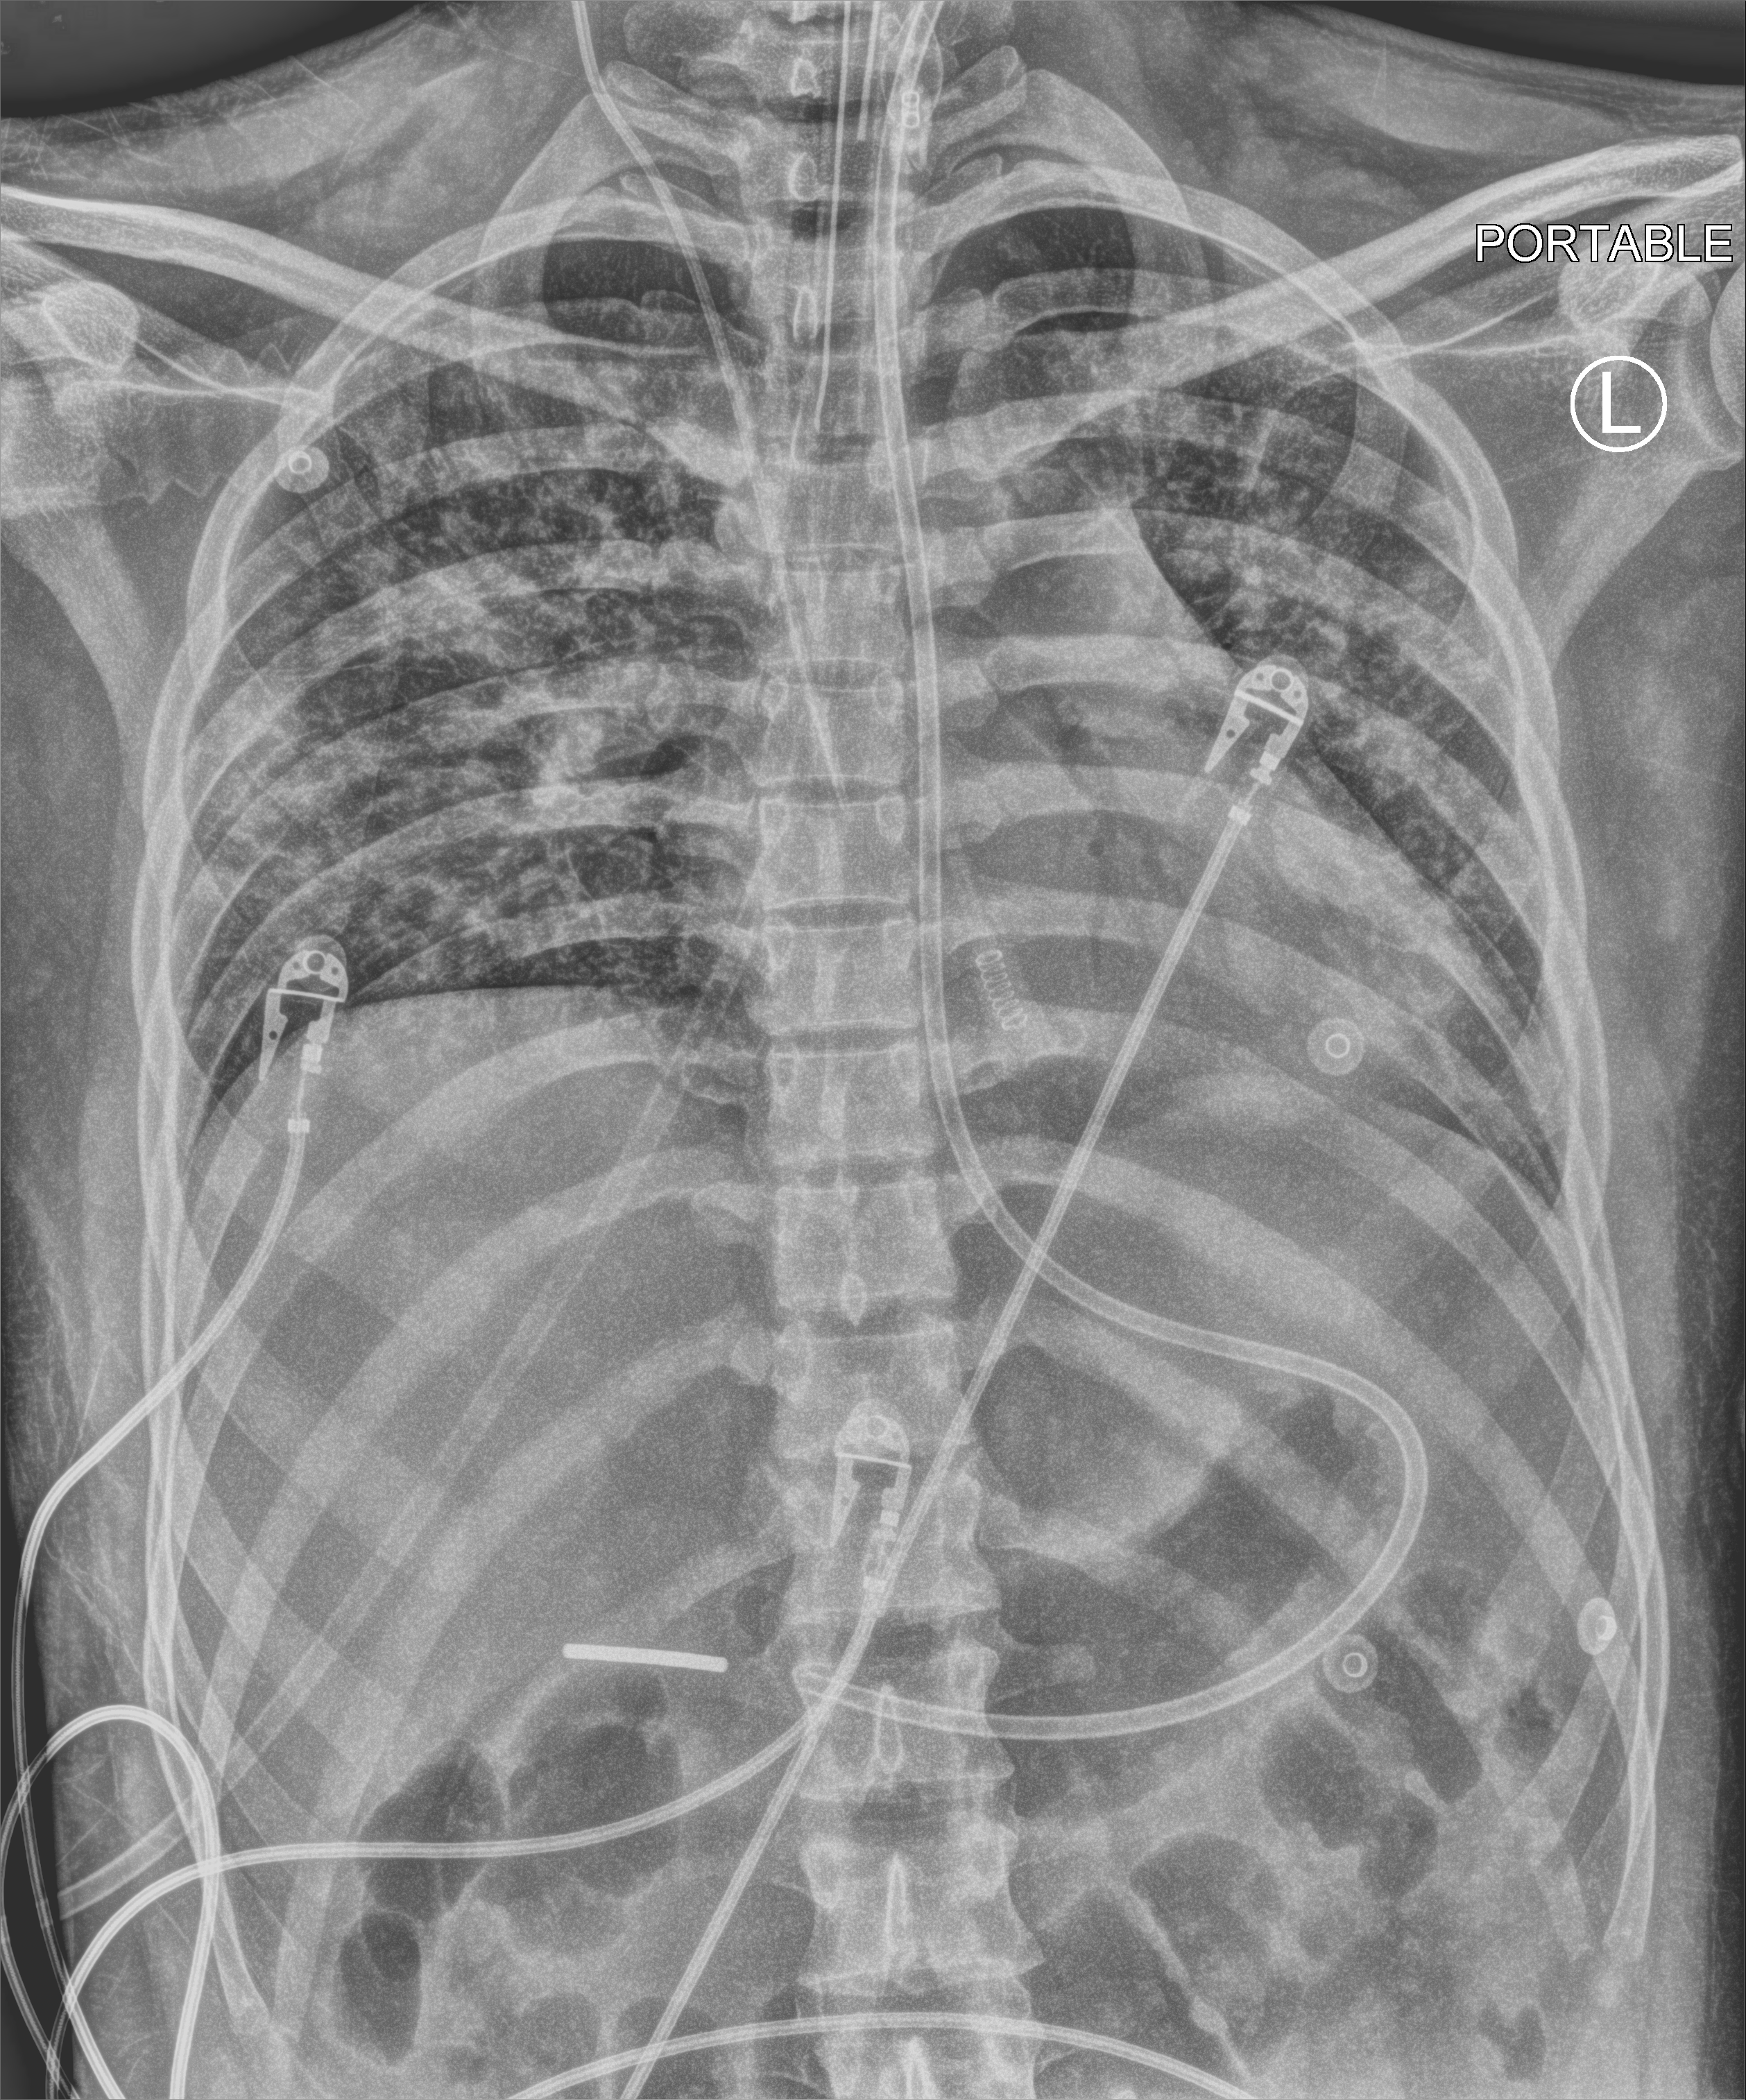
Bedside chest radiograph (computed radiography), anteroposterior (AP) projection. Patient hospitalised with COVID-19; male, aged 18–59 years.
Hospital-stay facts (about this admission, not read from this image; timing relative to this image not recorded):
- COPD (admission record): no